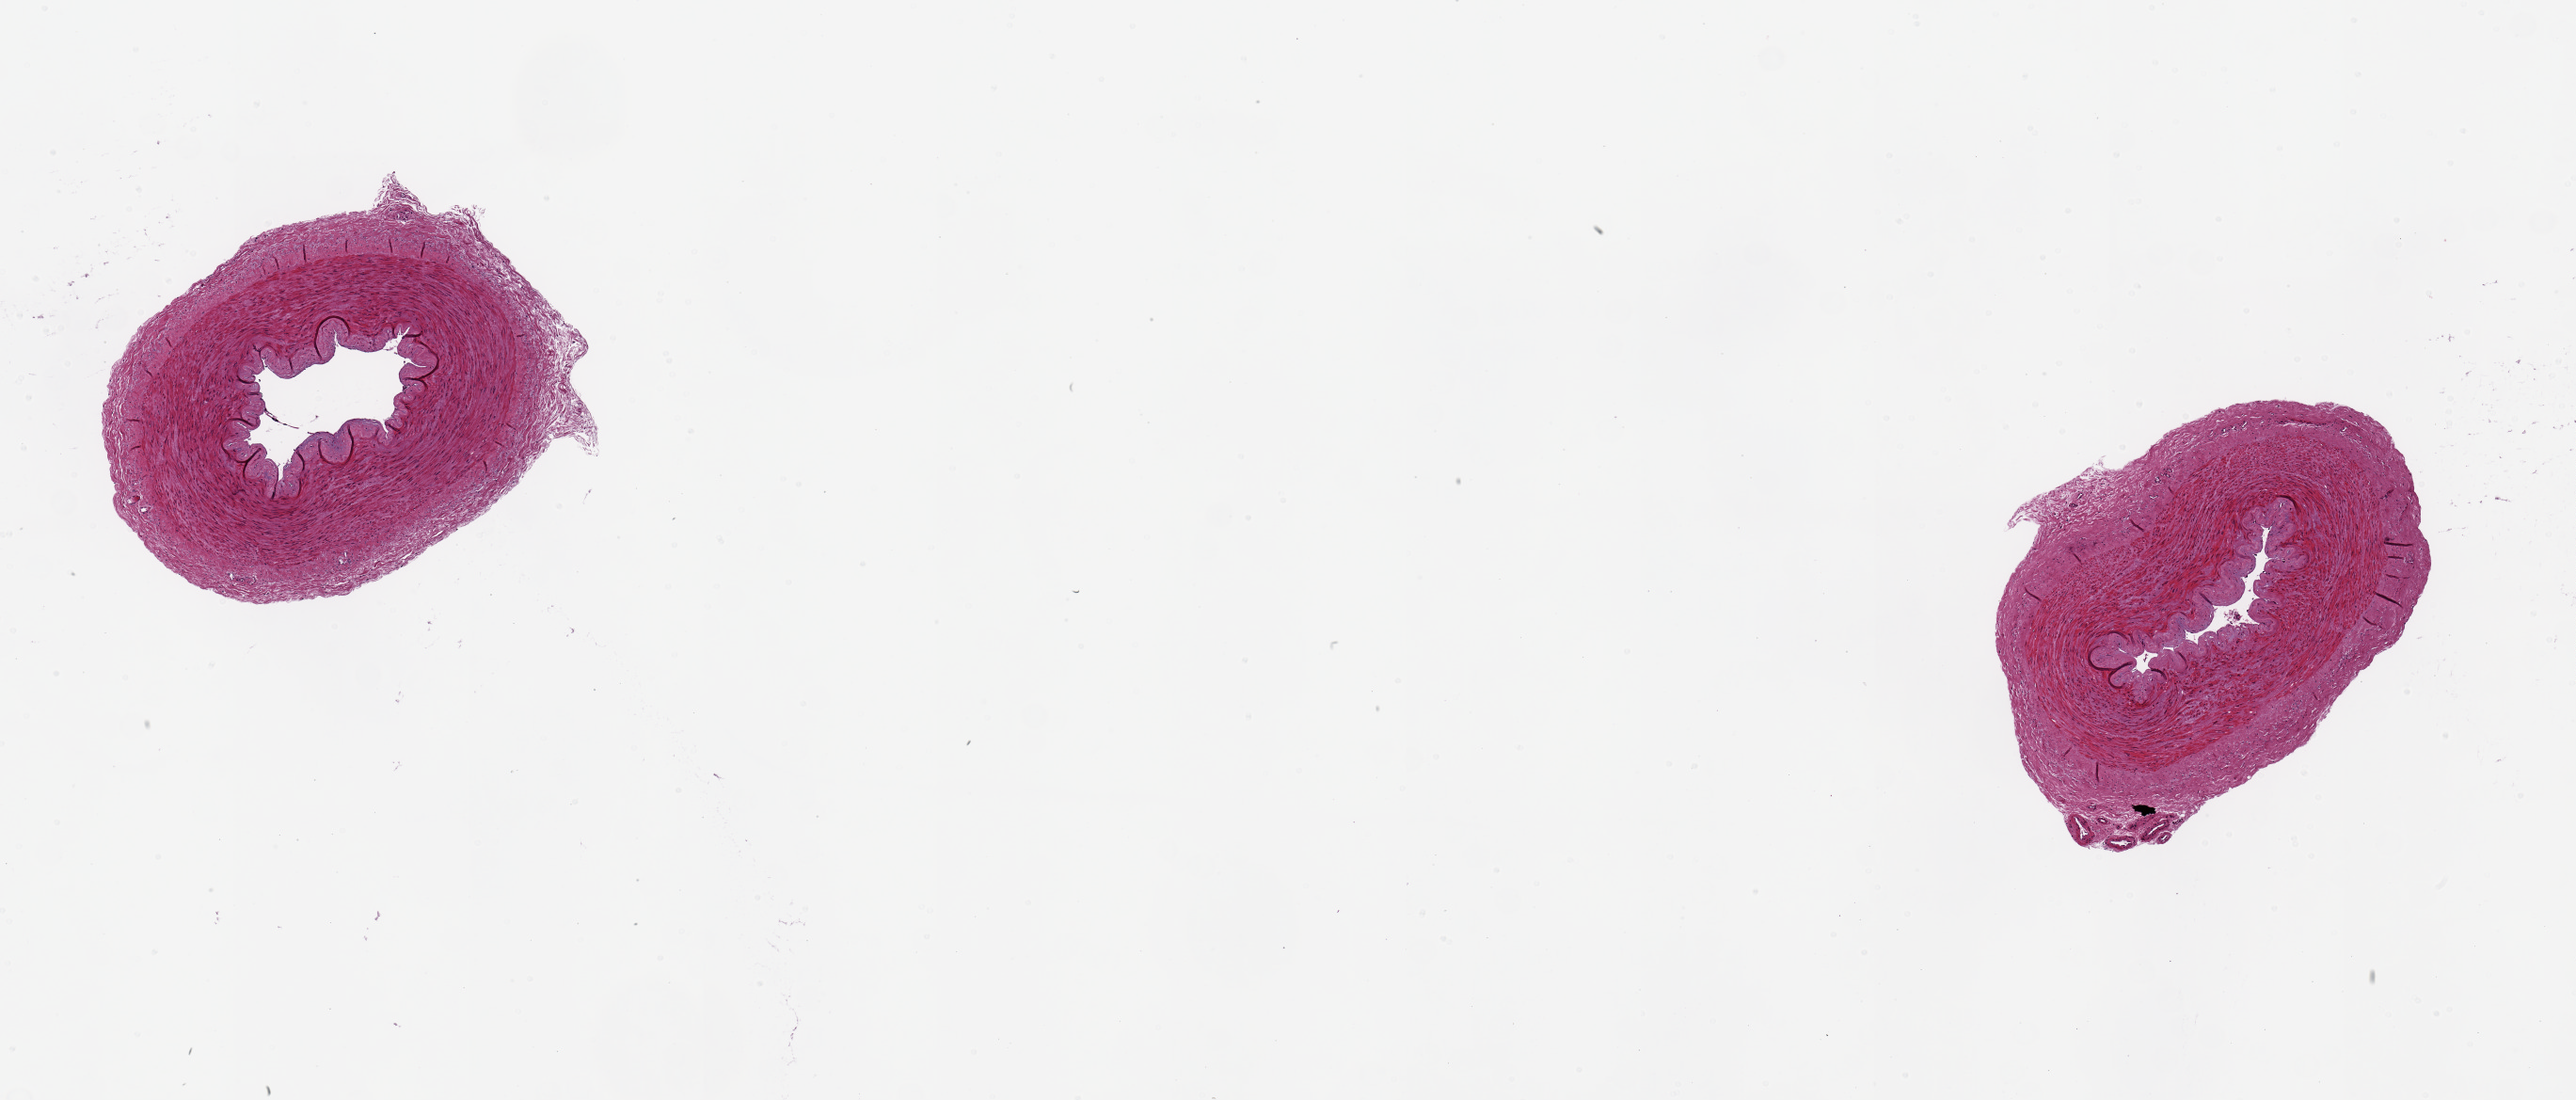
Hematoxylin and eosin (H&E) whole-slide image, brightfield, low-resolution overview of the scanned area, about 10.8 x 4.6 mm (slide scanned at 20x); PAXgene-fixed paraffin-embedded (PFPE) section; section of tibial artery (target tissue); tissue donor sample. Female donor.
Pathologist's review note for this sample: 2 pieces ~2mm d. Good clean specimens, no atherosis.